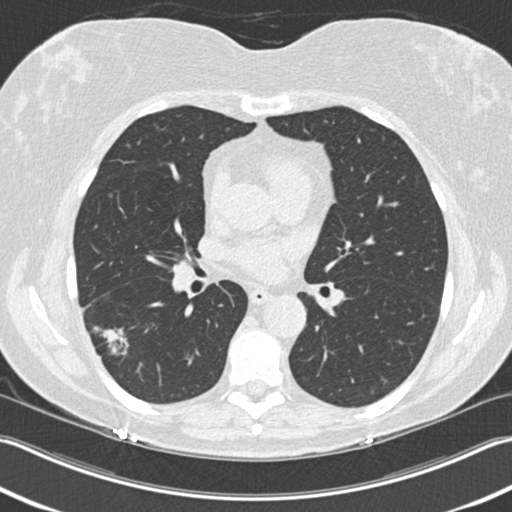
Axial slice from a low-dose chest CT screening exam. Baseline screening round. Lung window (W 1500 / L -600 HU). Standard (soft-tissue) reconstruction kernel (B30f). Slice 91 of 211 in the series. Female, age 63 years at enrolment.
Expert-annotated lung lesion, box from (x=83, y=318) to (x=143, y=372) px. The screening reader recorded 3 non-calcified nodules or masses ≥4 mm on this exam (right upper lobe, right lower lobe, right lower lobe); which of them this box marks is not recorded. Official screen result: positive, change unspecified: nodule(s) >= 4 mm or enlarging nodule(s), mass(es), or other non-specific abnormalities suspicious for lung cancer. Participant outcome: lung cancer diagnosed 57 days after this screen — bronchiolo-alveolar adenocarcinoma, NOS, right lower lobe, well differentiated (G1), stage IA (AJCC 6th edition), 25 mm at pathology.